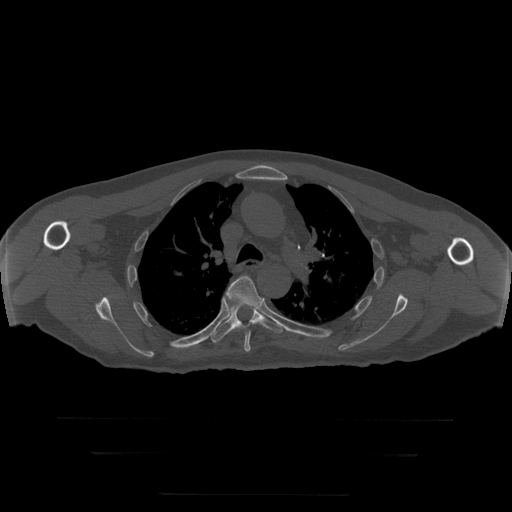
CT including the spine, one axial slice; slice 216 of 397 in the series (ordered by position); 120 kVp; bone window (W 1800 / L 400 HU); 1.25 mm slice thickness; 512 × 512 image matrix. Patient age 73 years. From the clinical record (not read from this slice): primary cancer: prostate.
Outlined on this slice (semi-automatically segmented with operator editing):
- T5 vertebra: bounding box (x1, y1, x2, y2) in pixels: (226, 276, 262, 352)
- T6 vertebra: (207, 297, 283, 343)